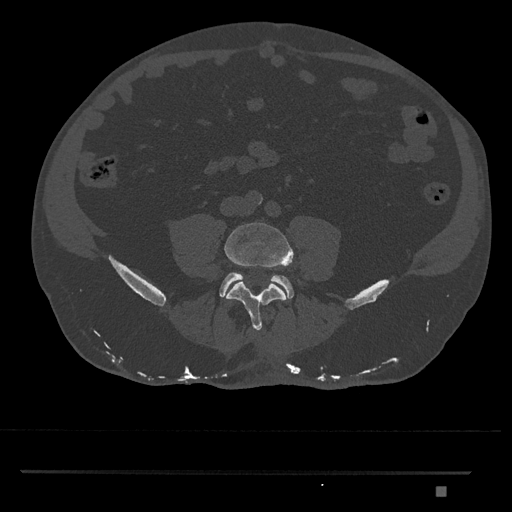
CT including the spine, one axial slice; slice 593 of 1134 in the series (ordered by position); reconstruction kernel Br40s/3; bone window (W 1800 / L 400 HU); 0.5 mm slice thickness; 512 × 512 image matrix, field of view 429 × 429 mm. Patient: male, 65 years. Case-level facts recorded for this patient, not image findings: primary cancer: prostate.
Structures marked on this image (semi-automatic segmentation, software-assisted and operator-edited):
- L4 vertebra: bounding box <224,222,294,331> (left, top, right, bottom; pixels)
- L5 vertebra: <219,272,294,299>